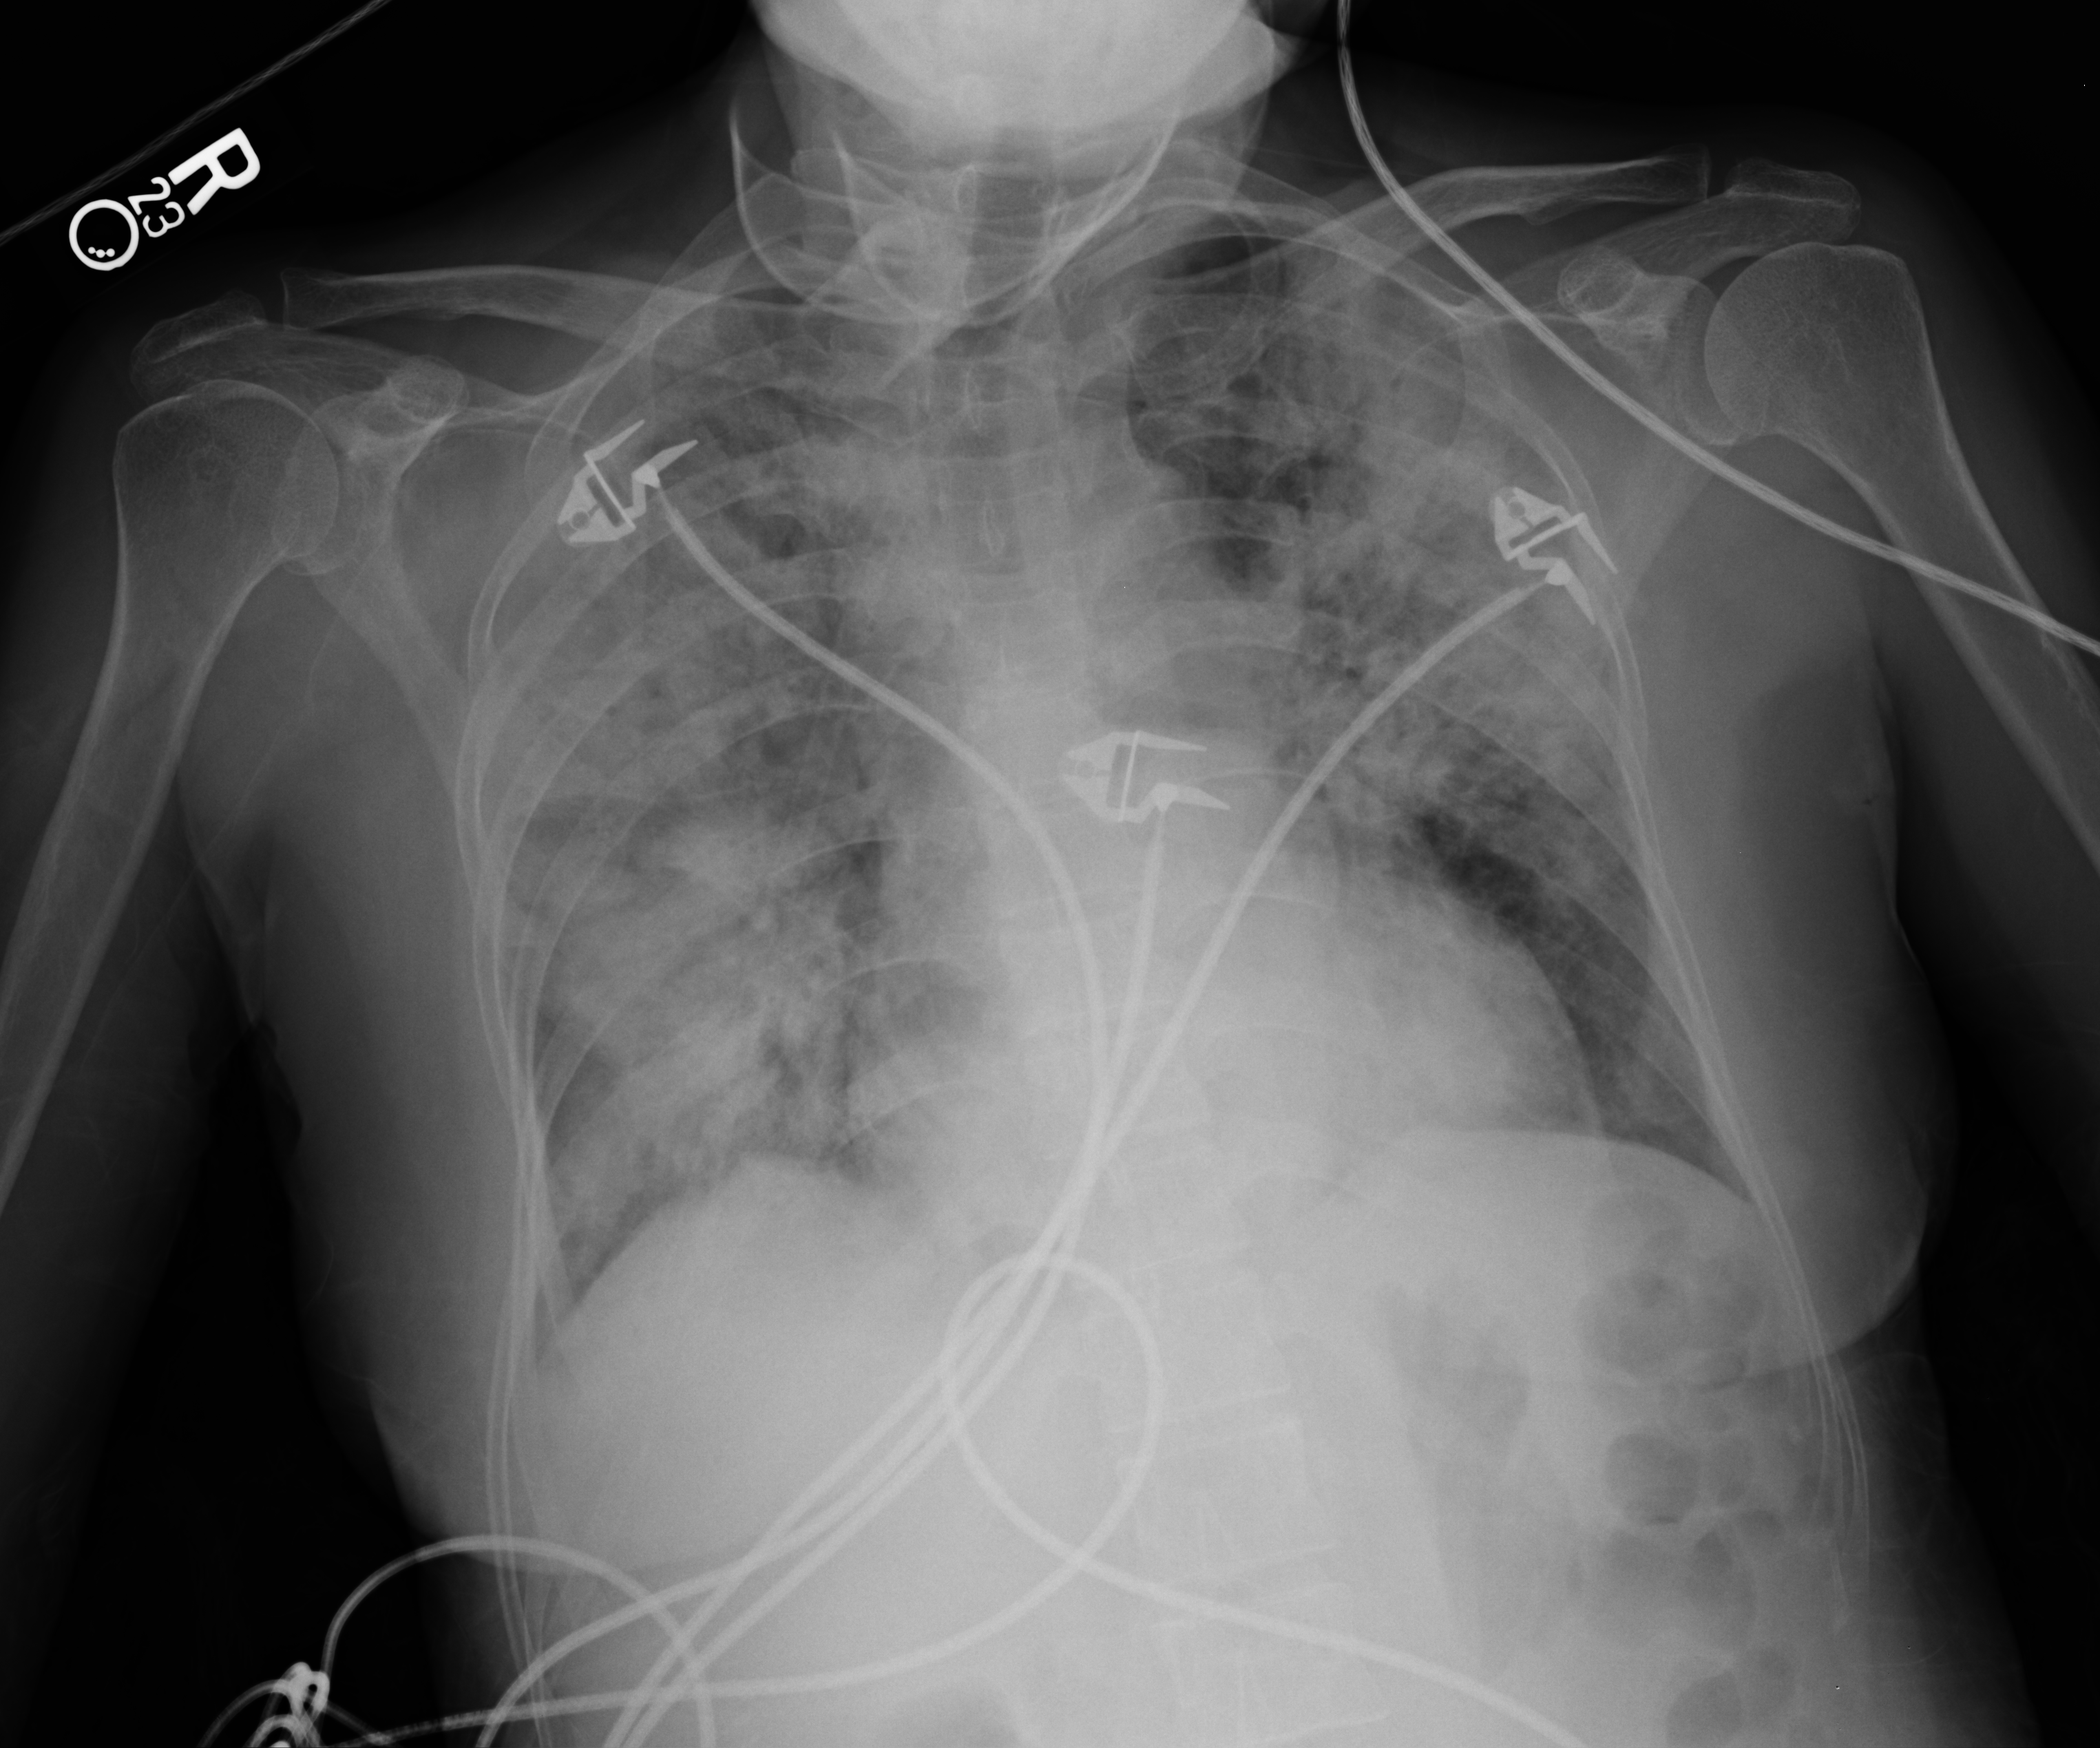
Portable chest radiograph; anteroposterior (AP) projection. Female patient hospitalised with COVID-19, age 60–74 years.
From the hospital-stay record, not from the radiograph (when in the stay this image was taken is not recorded): hypertension (admission record): no; other chronic lung disease (admission record): no.